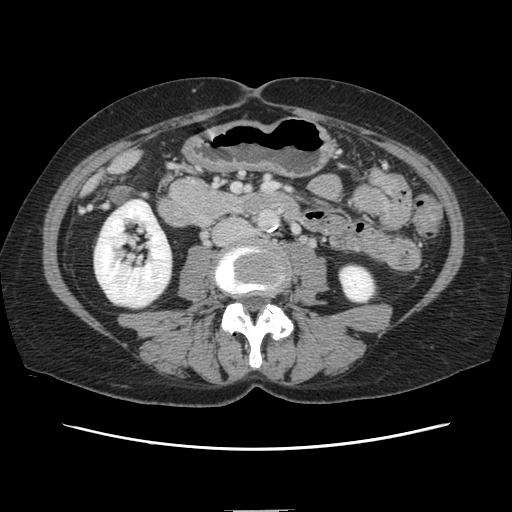
Contrast-enhanced abdominal CT, one axial slice; 120 kVp; intravenous contrast given; soft-tissue window (W 400 / L 40 HU); 2.5 mm slice thickness; 512 × 512 image matrix, field of view 350 × 350 mm. Female patient, age 63 years. From the clinical record (not read from this slice): diagnosis: colorectal cancer liver metastases, imaged before liver resection; multiple liver metastases: yes; largest metastasis: 3.2 cm; disease in both lobes: yes.
Annotated regions visible in this slice (manually delineated by an expert):
- liver: bounding box (x1, y1, x2, y2) in pixels: (89, 155, 136, 188)